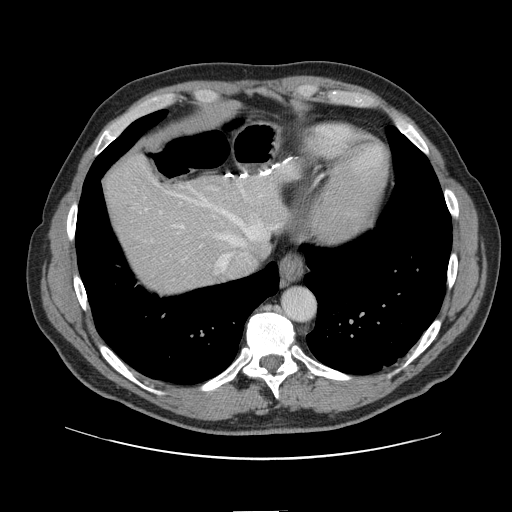
Contrast-enhanced abdominal CT, one axial slice. Slice 126 of 161 in the series (ordered by position). 120 kVp. Intravenous contrast given. Soft-tissue window (W 400 / L 40 HU). 512 × 512 image matrix, field of view 412 × 412 mm. Male patient, age 66 years. From the clinical record (not read from this slice): diagnosis: colorectal cancer liver metastases, imaged before liver resection; multiple liver metastases: no; largest metastasis: 3.5 cm; disease in both lobes: no.
Structures marked on this image (outlined manually by an expert reader):
- hepatic veins: bounding box <145,180,278,273> (left, top, right, bottom; pixels)
- liver: <105,157,294,293>
- planned liver remnant (the part of the liver to remain after resection): <106,158,294,289>